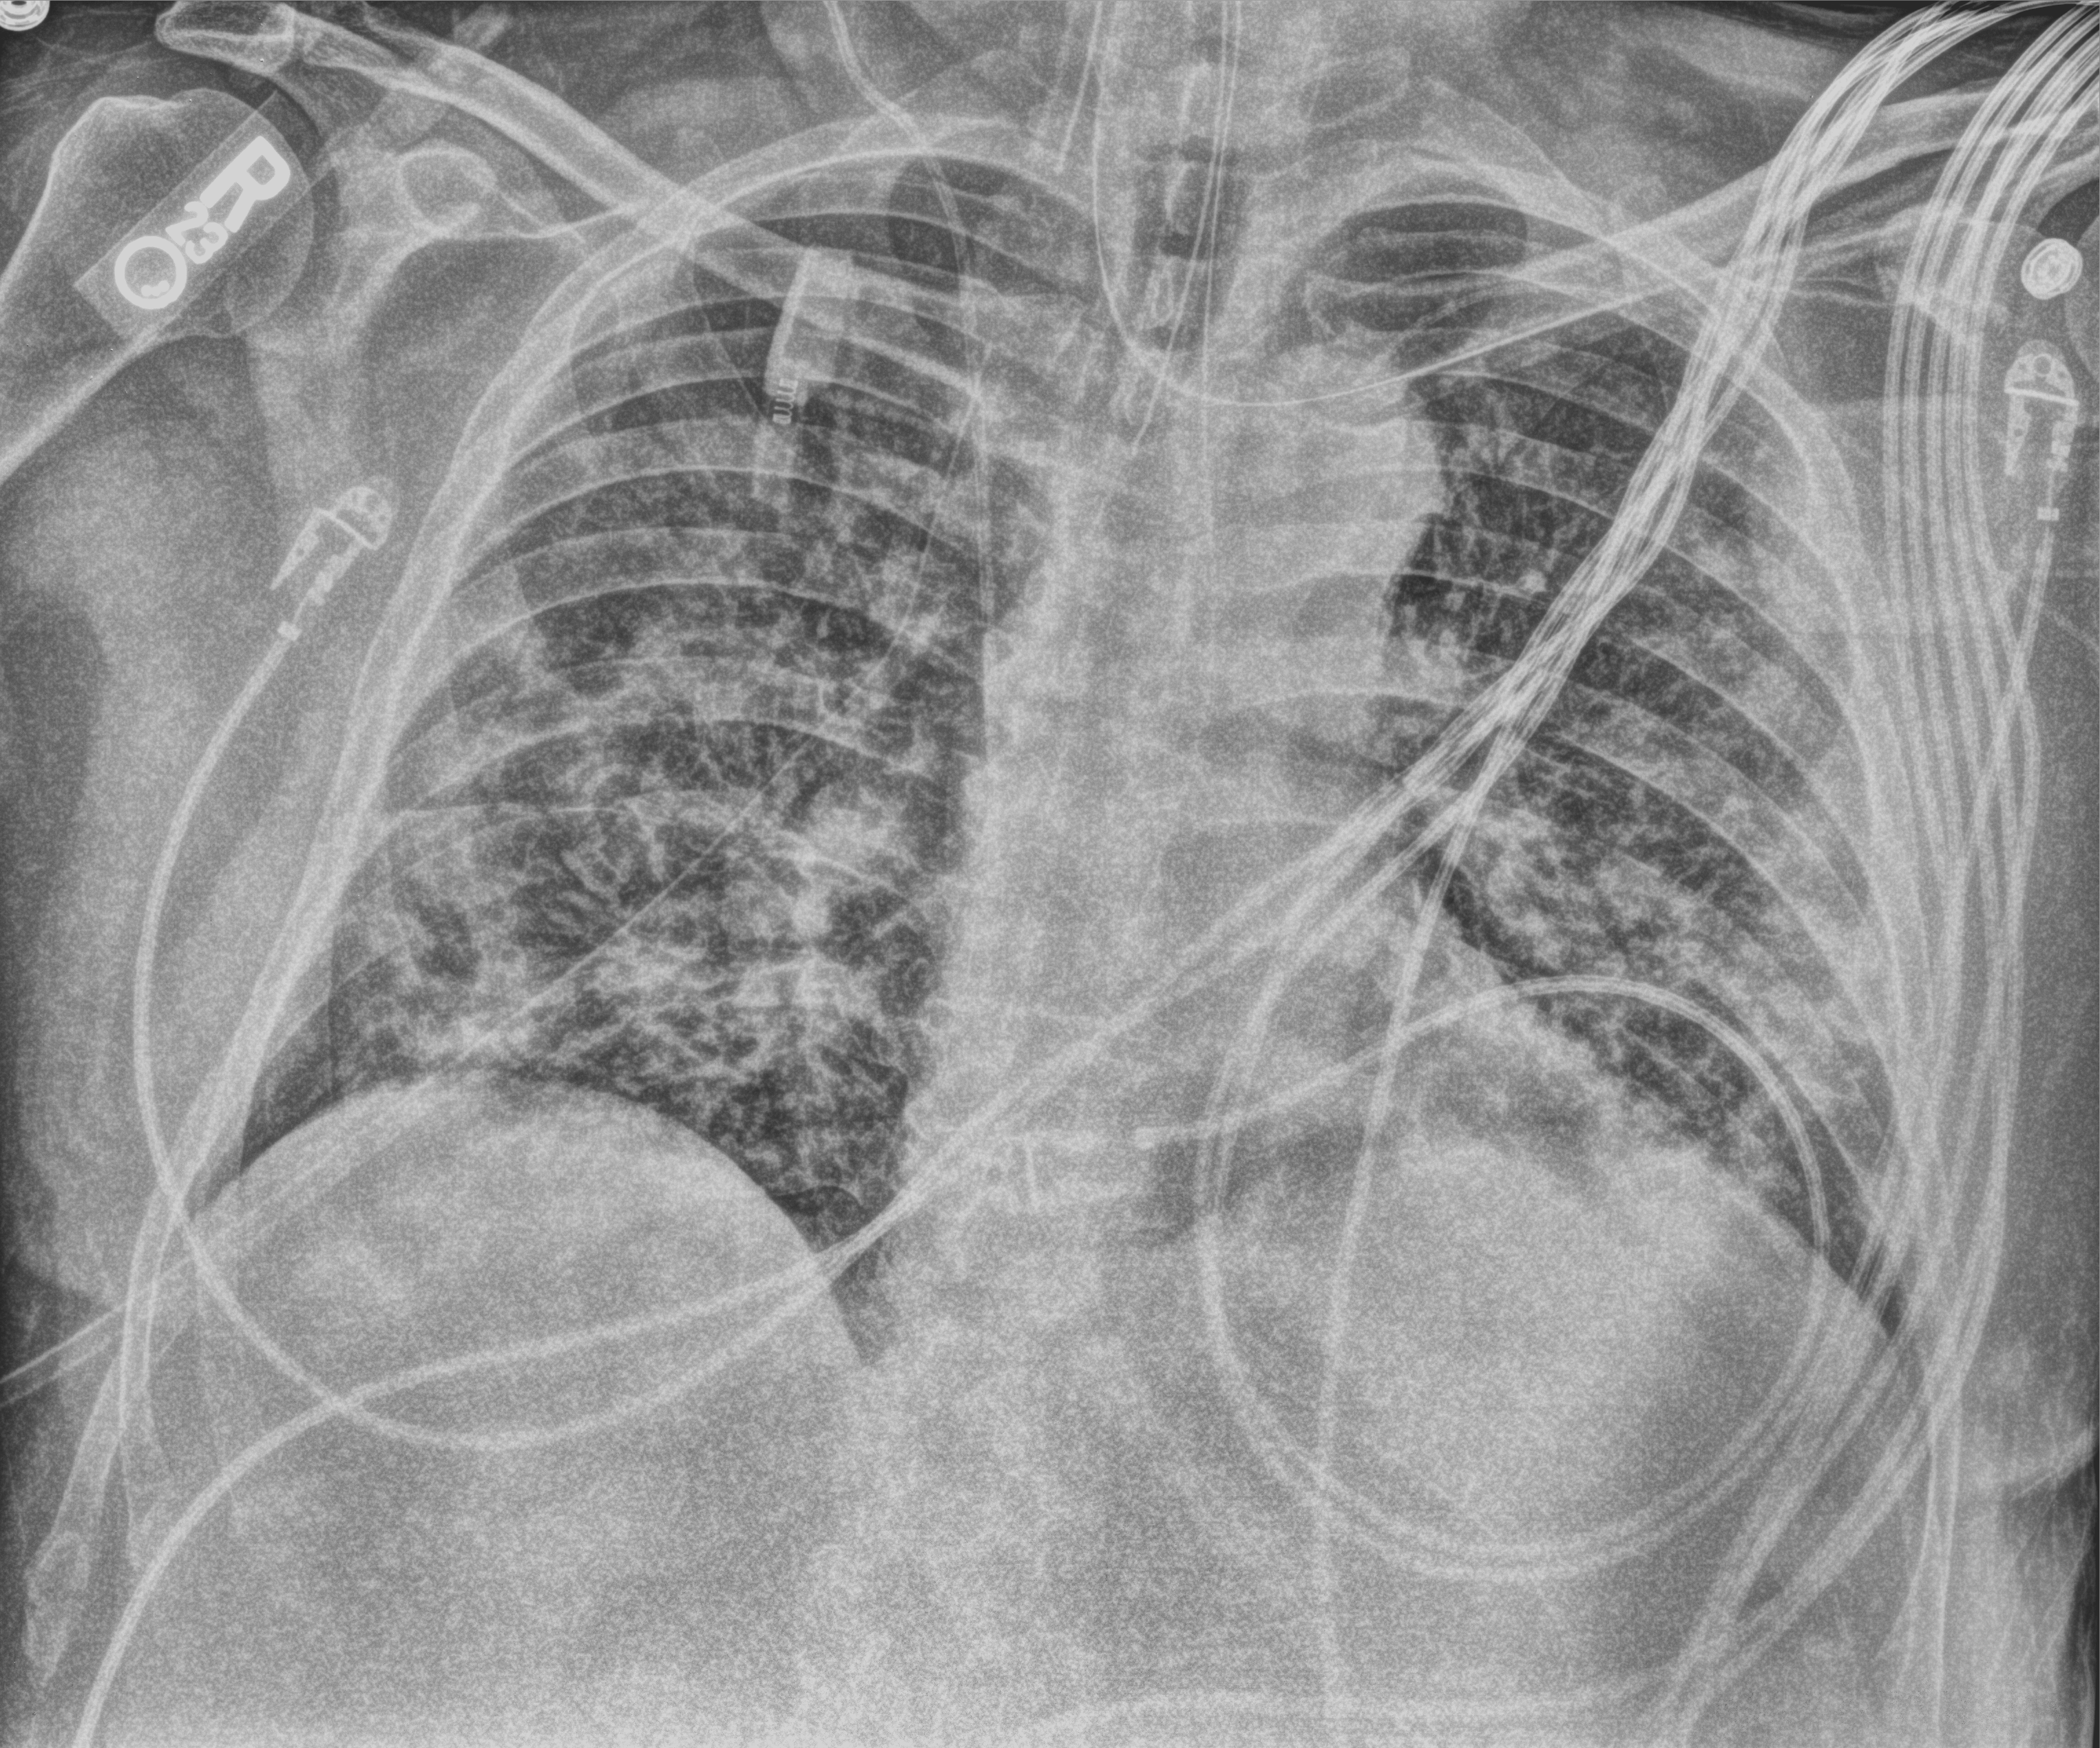
Bedside chest radiograph (computed radiography); anteroposterior (AP) projection. Male patient hospitalised with COVID-19, age 60–74 years.
Hospital-stay facts (about this admission, not read from this image; timing relative to this image not recorded):
- admitted to intensive care during this hospital stay: yes